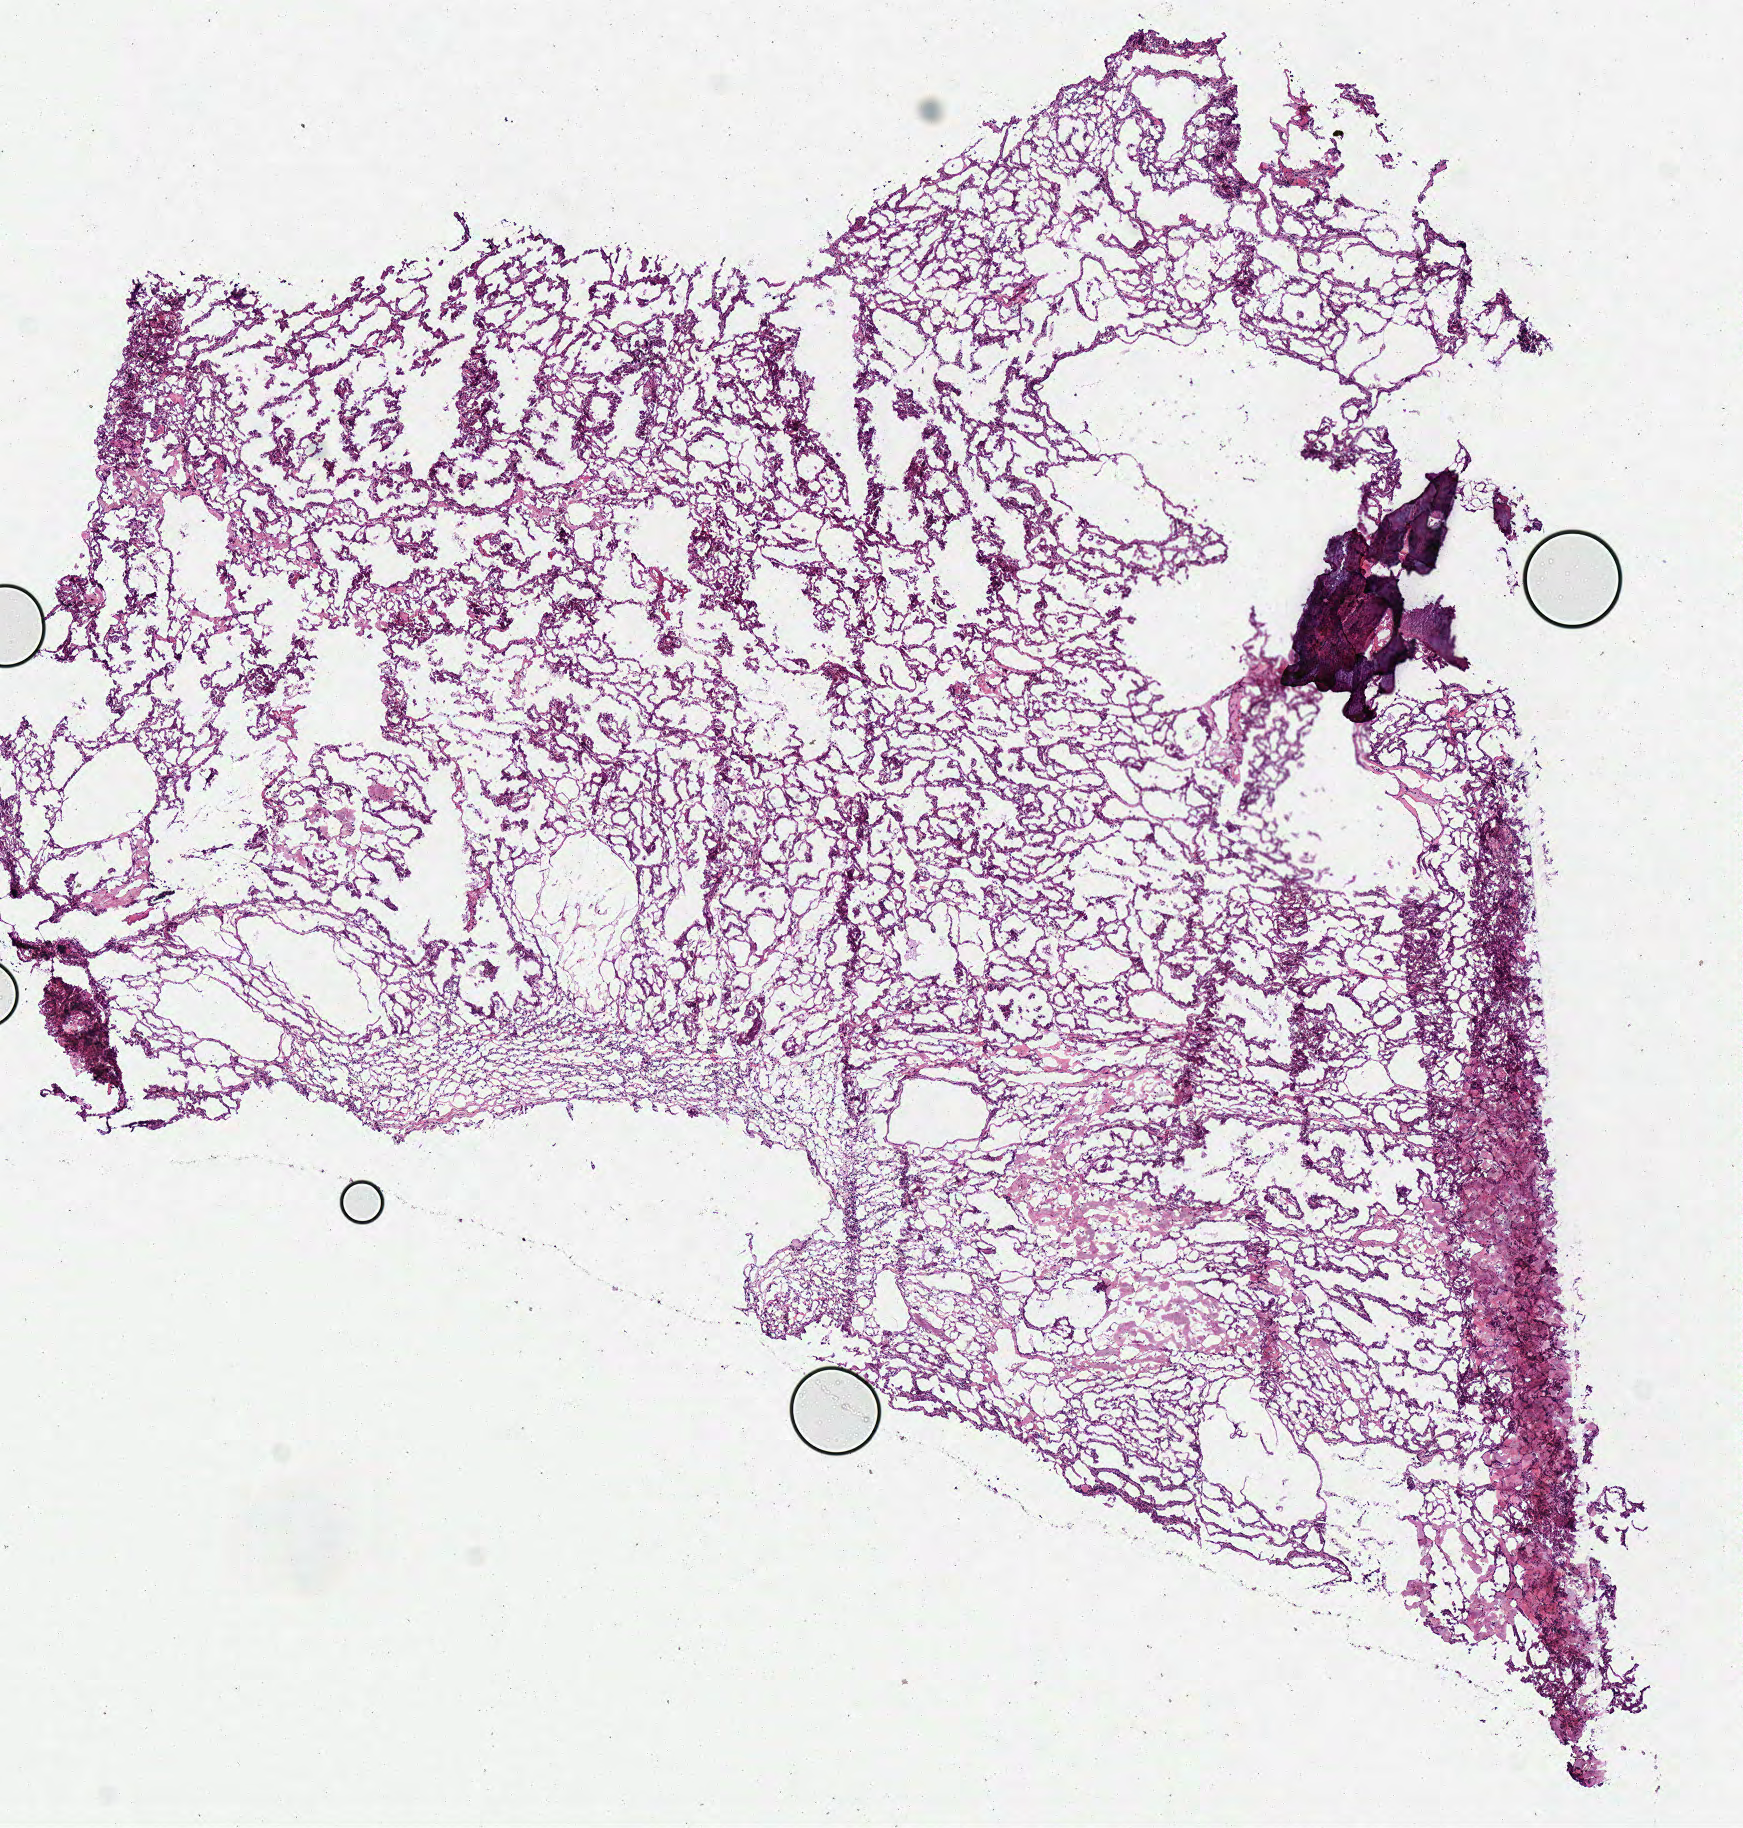
Whole-slide histology image, H&E-stained — shown as a low-resolution overview of the whole scanned area (about 6.9 x 7.2 mm, acquisition: 40x scan). Frozen section from the bottom of the tissue portion. Kidney, primary tumour sample. Patient: male, age at initial diagnosis 58 years. Slide review estimates, as recorded: tumour cells 90%, tumour nuclei 80%, normal cells 0%, stromal cells 10%, necrosis 0%.
- histologic diagnosis: Papillary adenocarcinoma, NOS
- AJCC pathologic stage: I (6th edition)
- laterality: left